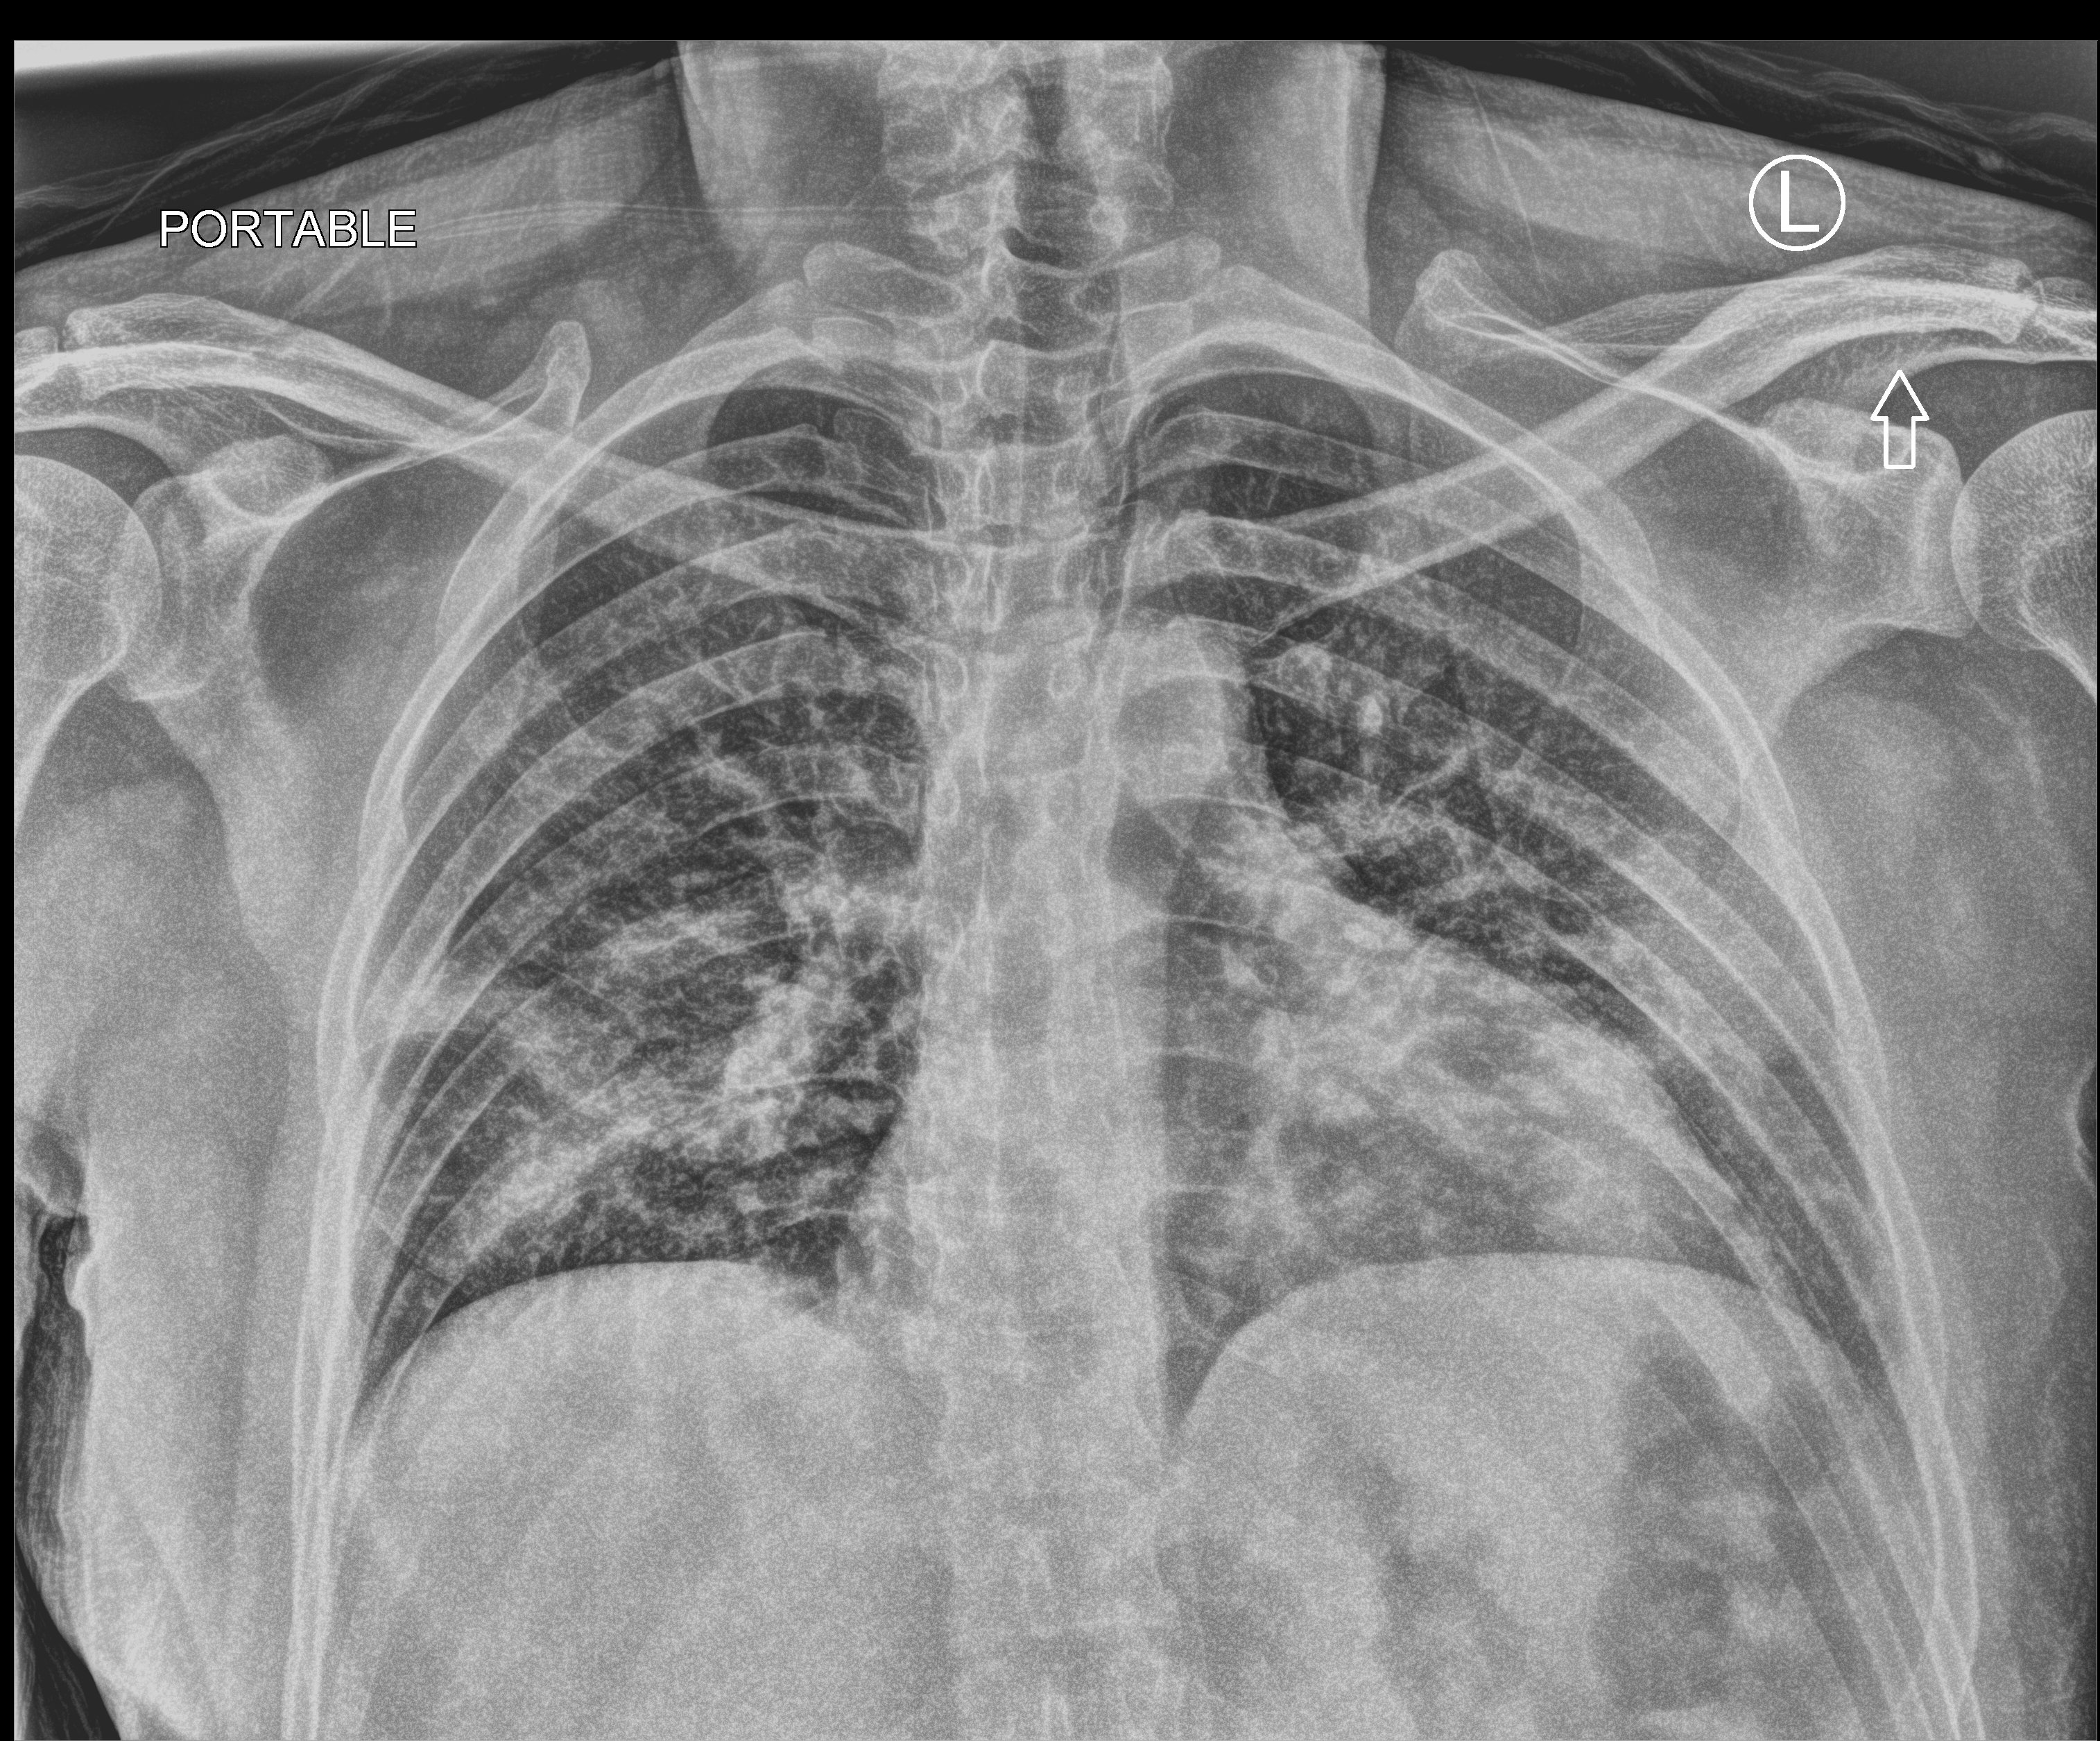
Chest X-ray (portable), anteroposterior (AP) projection. Patient hospitalised with COVID-19; male, aged 18–59 years.
Hospital-stay facts (about this admission, not read from this image; timing relative to this image not recorded): admitted to intensive care during this hospital stay: no.